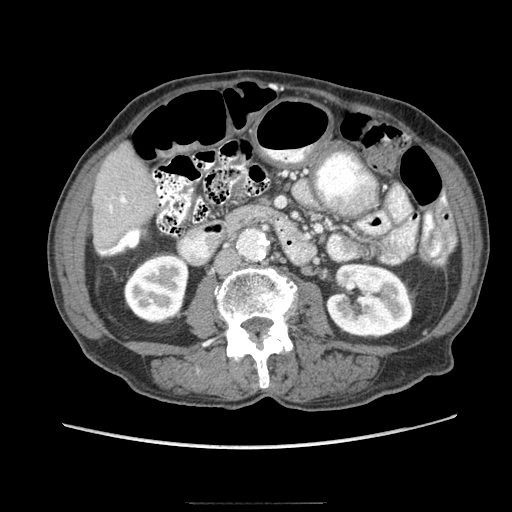
Contrast-enhanced abdominal CT (liver protocol), one axial slice; slice 20 of 83 in the series (ordered by position); reconstruction kernel STANDARD; 140 kVp; soft-tissue window (W 400 / L 40 HU); 2.5 mm slice thickness; 512 × 512 image matrix, field of view 360 × 360 mm. Case-level facts recorded for this patient, not image findings: diagnosis: hepatocellular carcinoma (patient treated with transarterial chemoembolisation; whether this scan precedes or follows treatment is not stated here); TNM stage (as recorded): Stage-I; Child-Pugh class: A; tumour differentiation: moderately differentiated; tumour nodularity: uninodular.
Outlined on this slice (semi-automatically segmented with operator editing):
- liver parenchyma outside the tumour (the mass and vessels are separate outlines, so this box may not span the whole liver): bounding box [x1, y1, x2, y2] px = [92, 144, 156, 256]
- liver vessels: [100, 195, 127, 254]